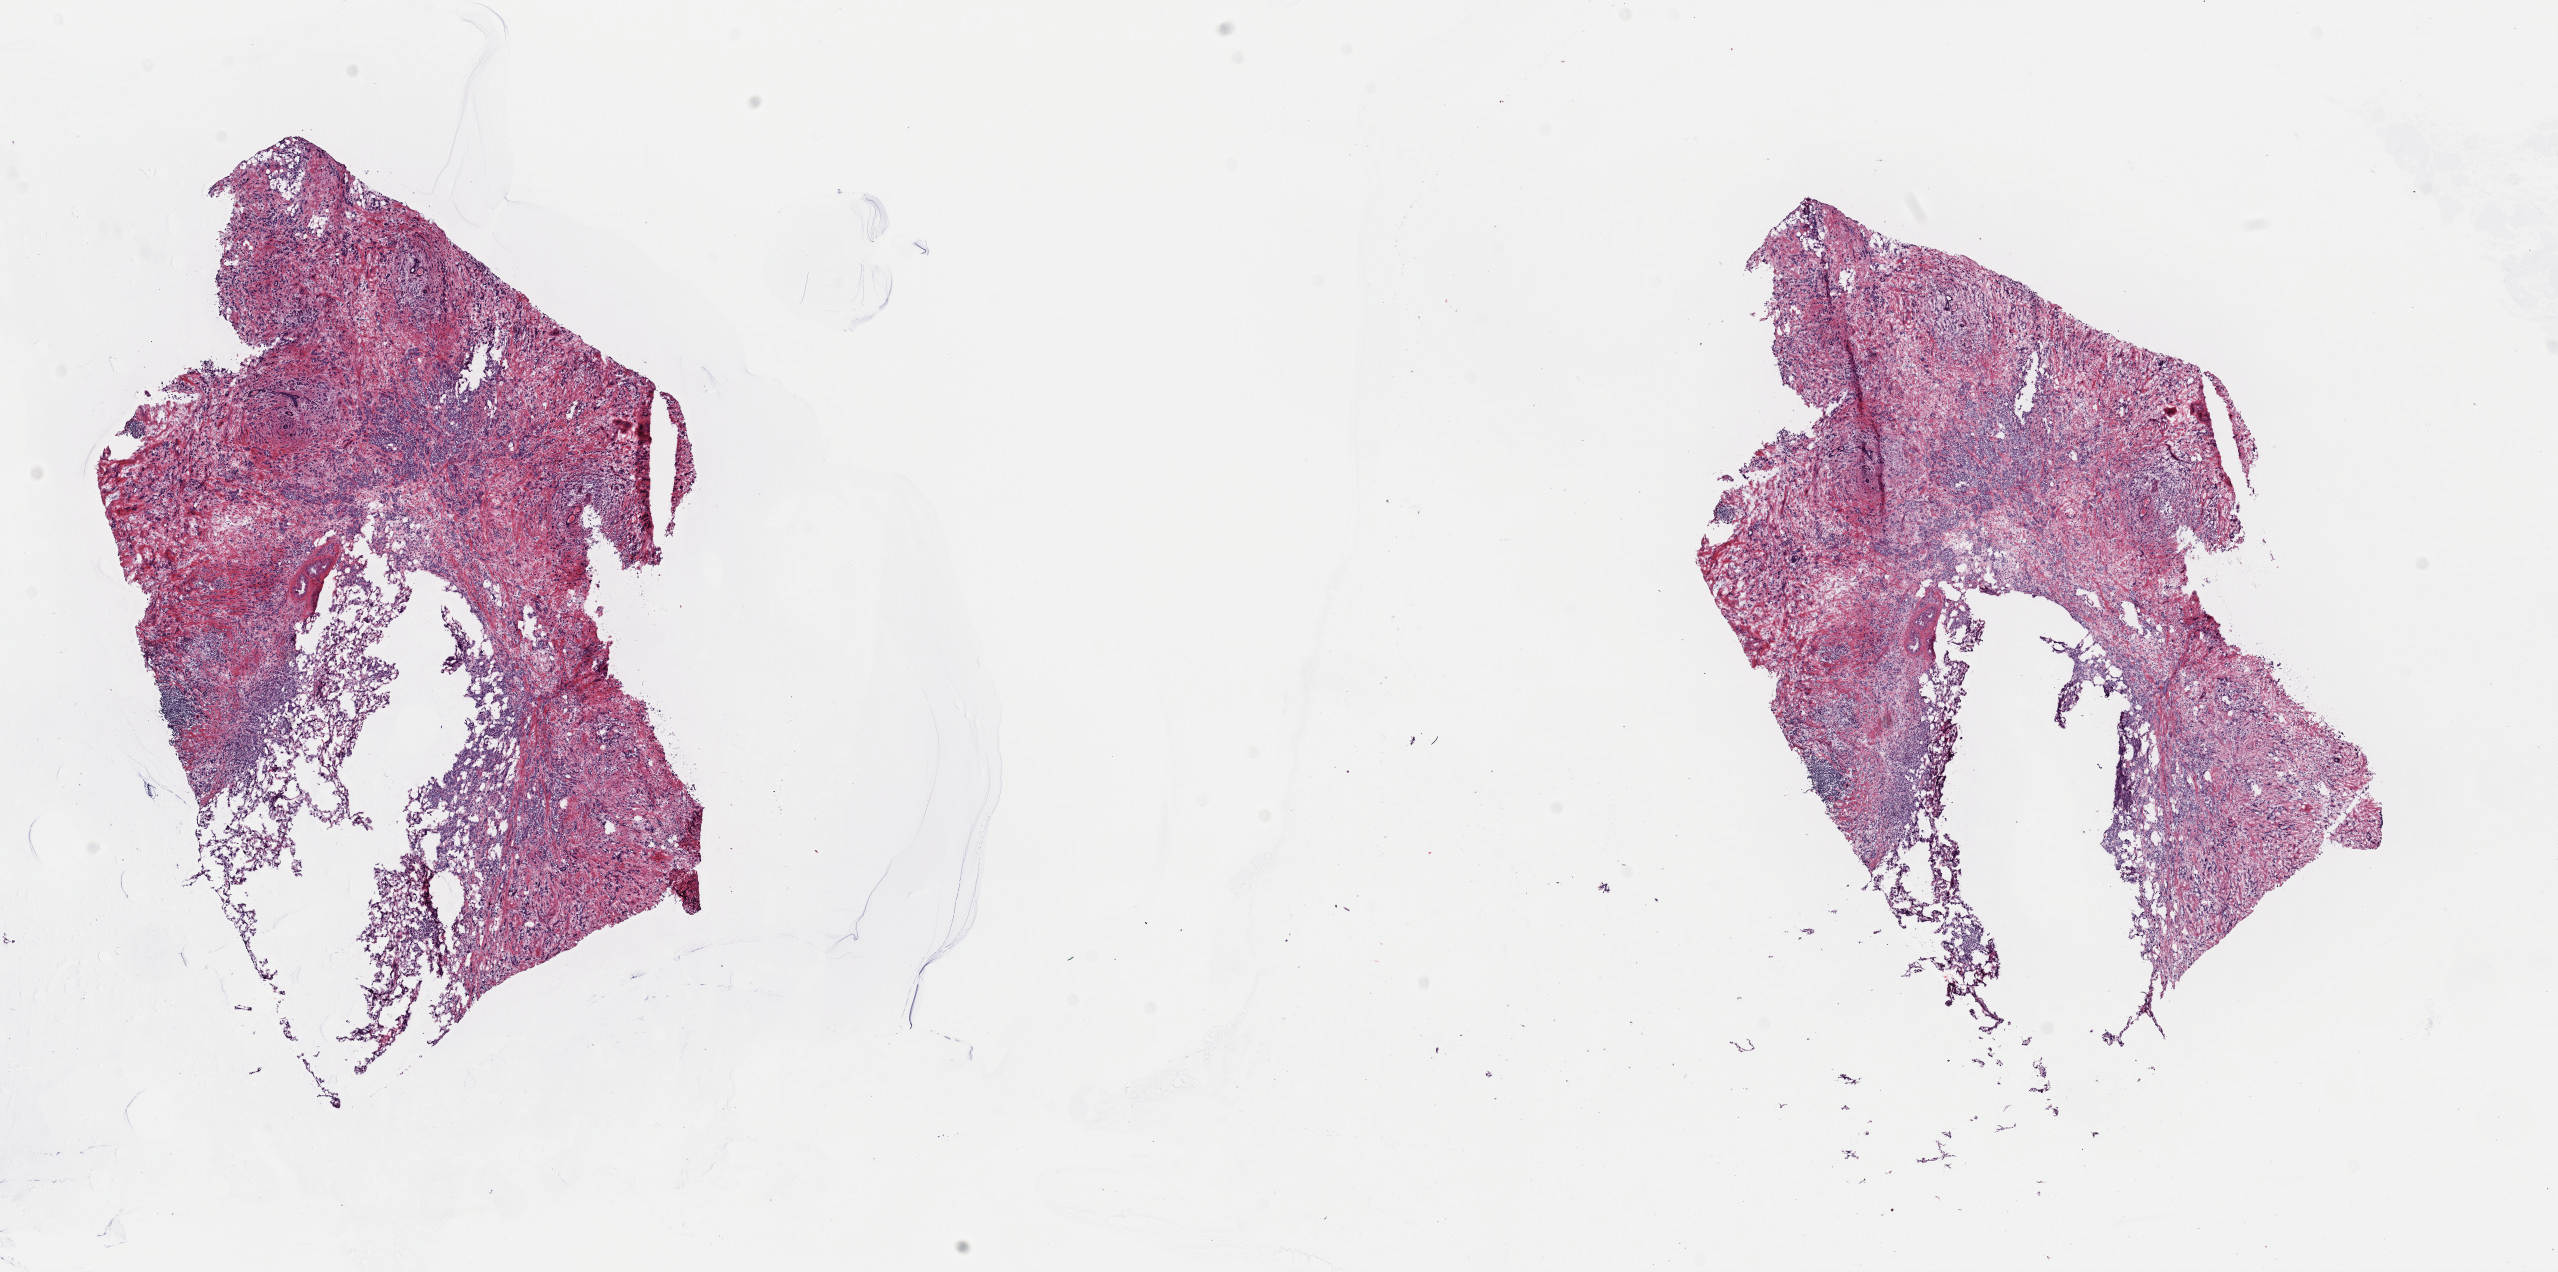
Hematoxylin and eosin (H&E) stained whole-slide image — shown as a low-resolution overview of the whole scanned area (about 20.2 x 10.0 mm), frozen section, primary tumour sample from the breast. Female, age 40 years at initial diagnosis. Composition of this section per pathologist review: tumour cells 55%, tumour nuclei 75%, normal cells 0%, stromal cells 45%, necrosis 0%. Infiltration values recorded for this section: lymphocyte infiltration 5%, monocyte infiltration 0%, neutrophil infiltration 0%.
Lymph nodes positive (case pathology): 1 of 10 examined. AJCC pathologic stage: IIB (7th edition). Laterality: left. Pathologic diagnosis: Lobular carcinoma, NOS.